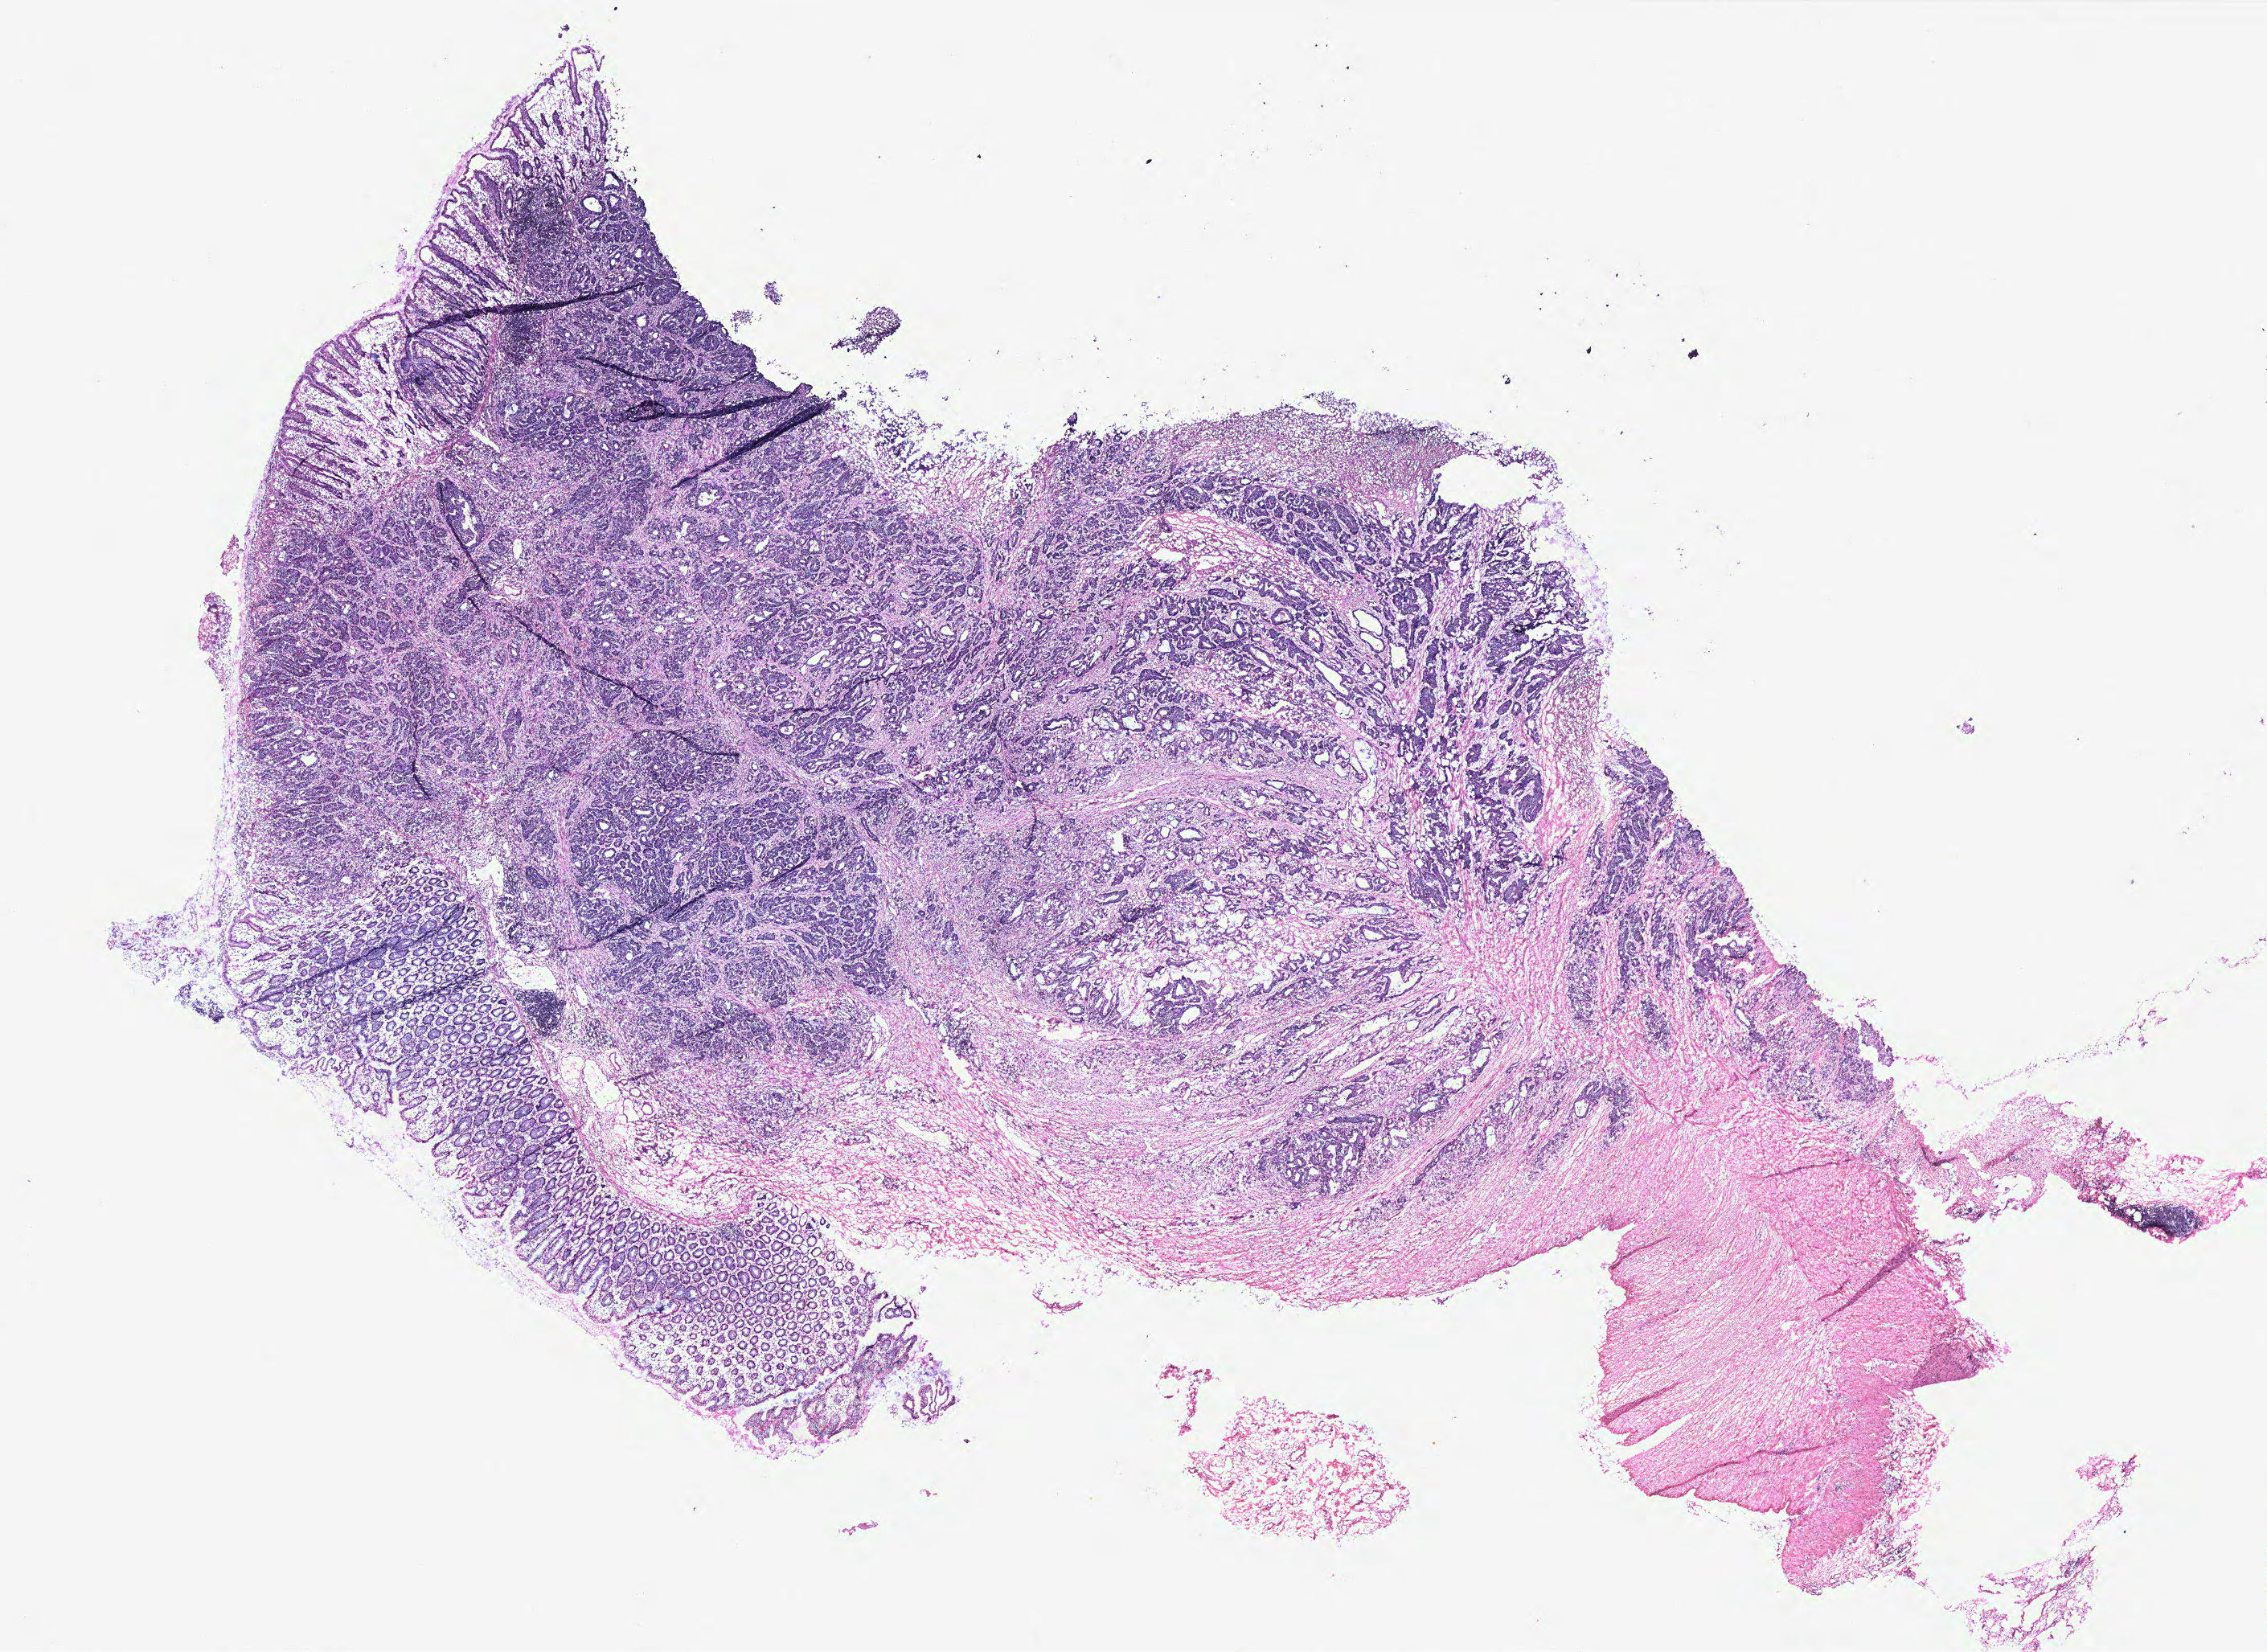
Whole-slide histology image, H&E — whole scanned area (about 22.6 x 16.4 mm) shown as a low-resolution overview. Colon, tissue type not recorded.
Patient diagnosis (cohort enrolment): colon cancer (colon).